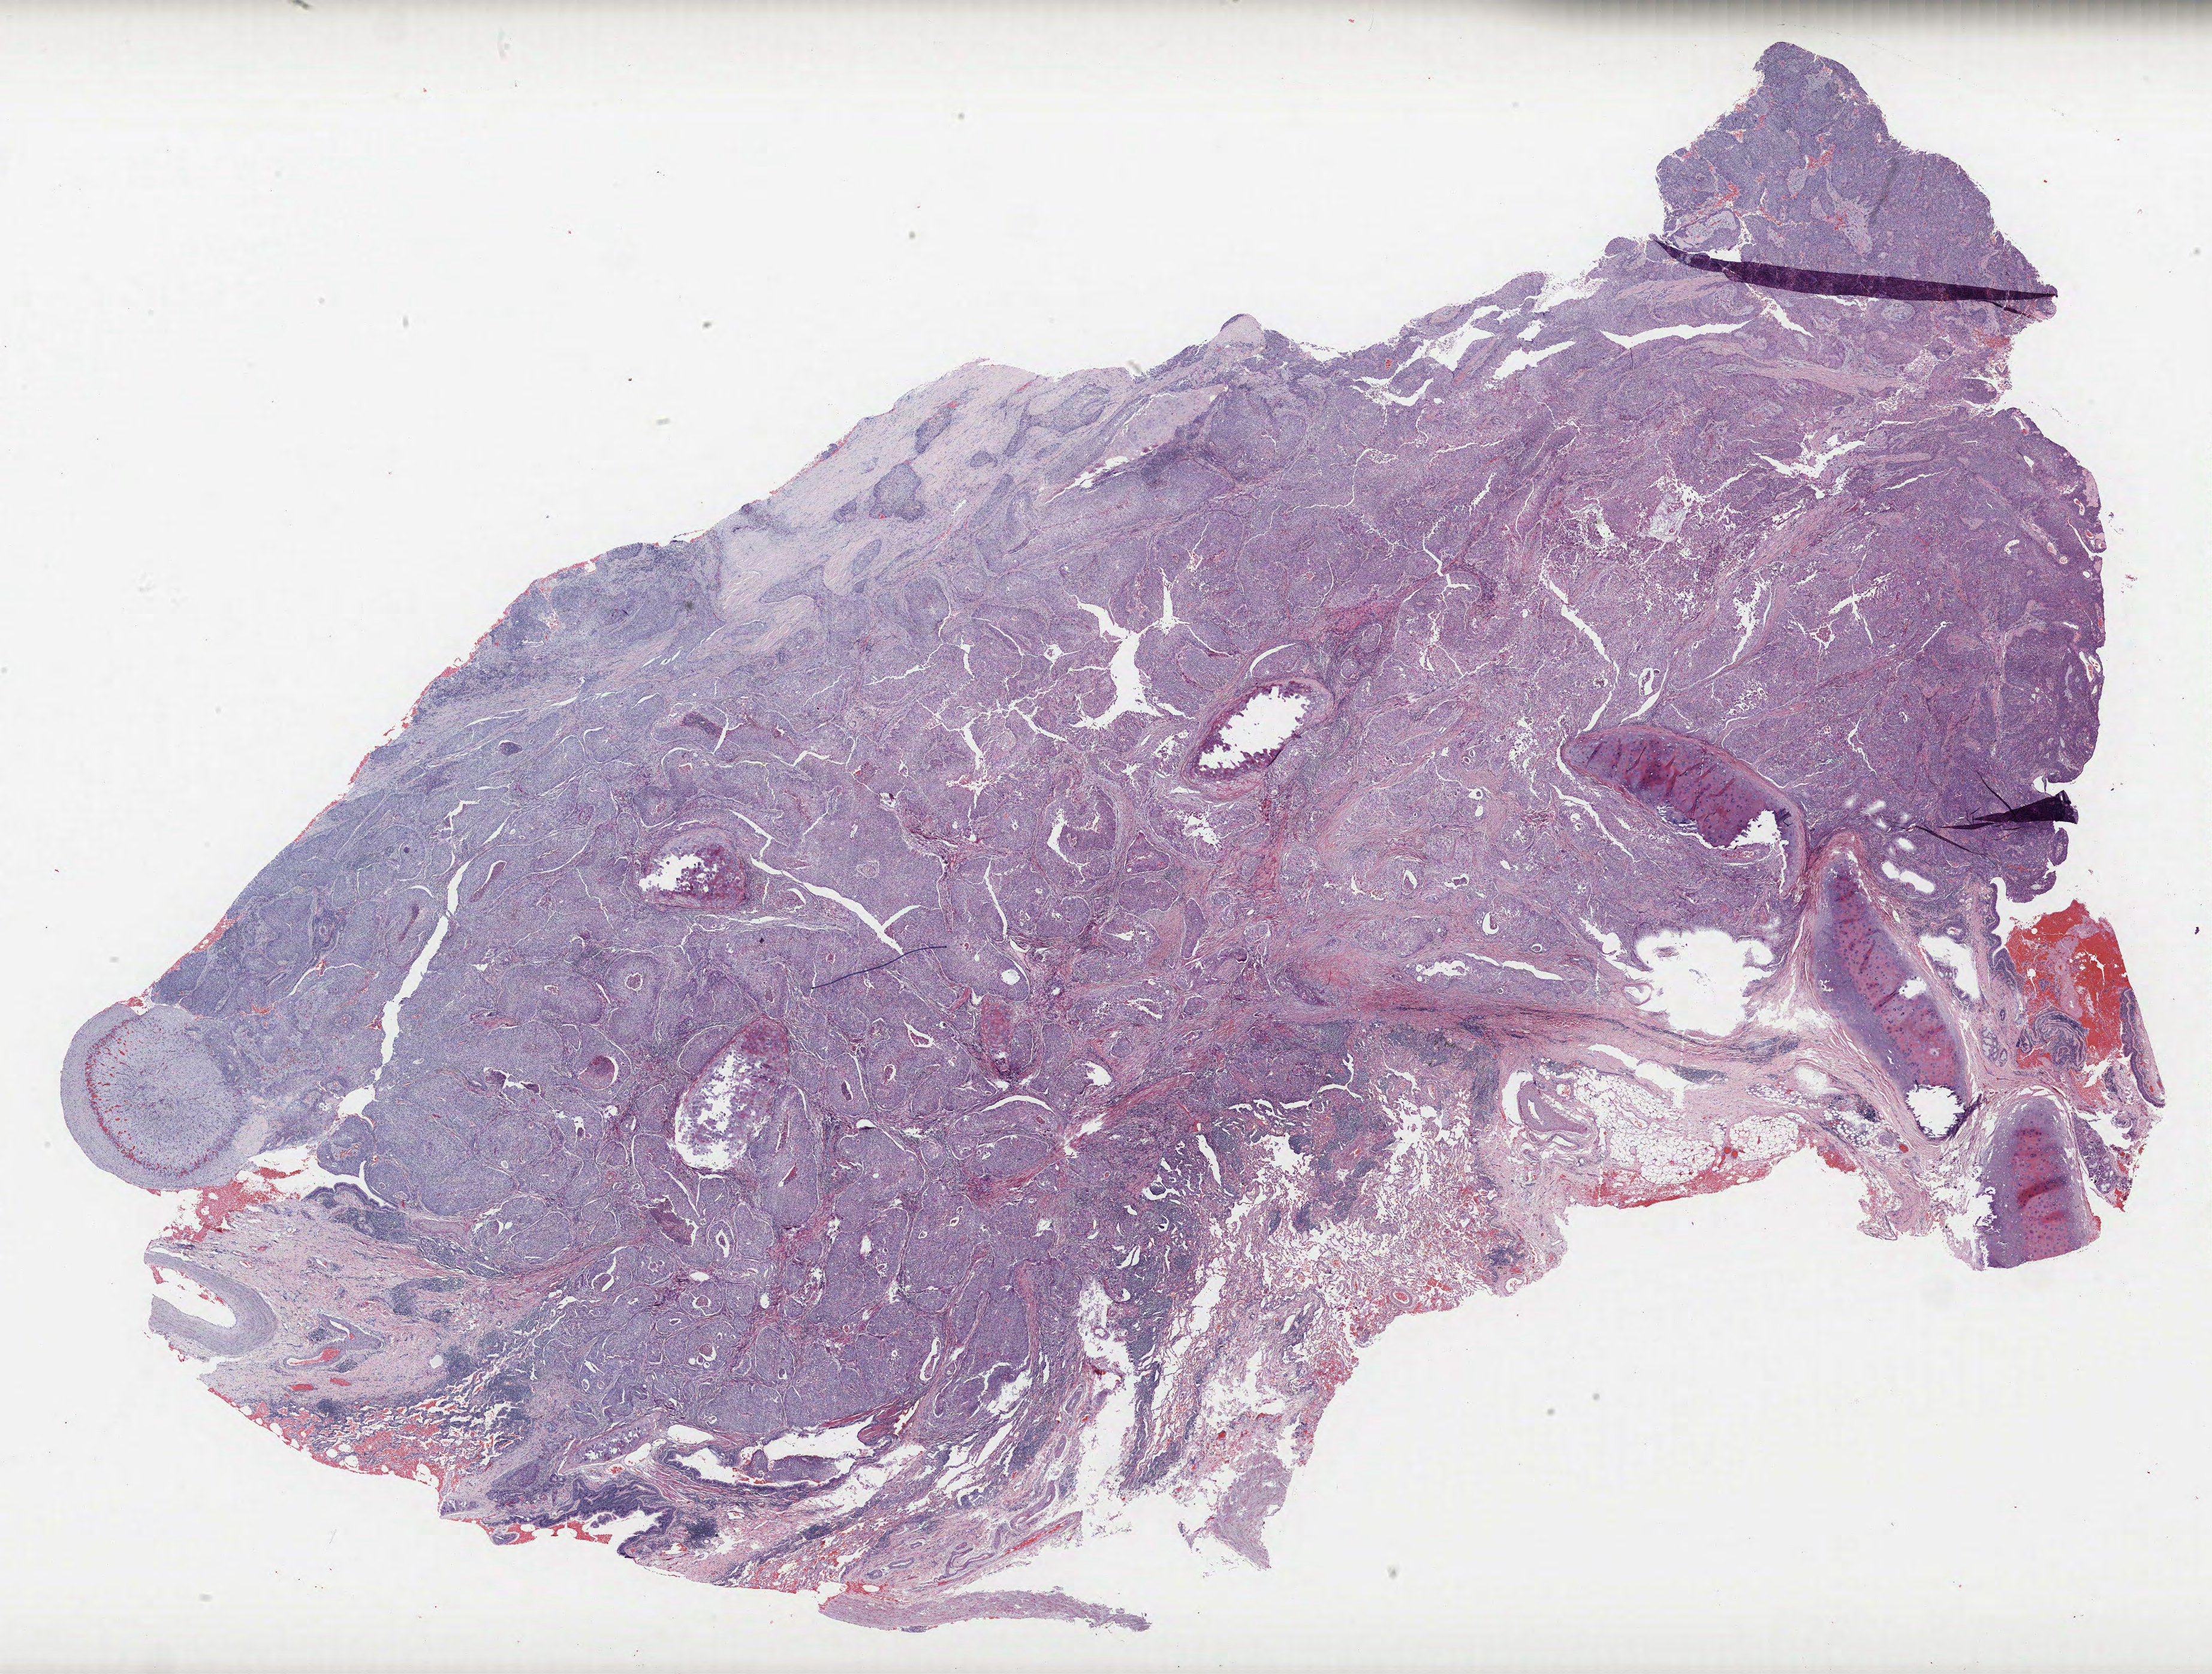
Whole-slide histology image, H&E — low-resolution overview of the scanned area, about 29.5 x 22.3 mm (slide scanned at 40x); formalin-fixed paraffin-embedded (FFPE) section; lung. Male, age 72 at enrolment. Former smoker at enrolment. Grade: poorly differentiated (G3).
Participant's lung-cancer diagnosis: Squamous cell carcinoma, NOS (ICD-O-3 8070/3). Stage (AJCC 6th edition): IA. Tumour size (pathology): 30 mm. Primary tumour location (clinical record): right upper lobe.